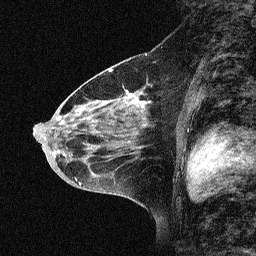
Breast MRI (dynamic contrast-enhanced), one sagittal slice; slice 35 of 64 in the series (ordered by position); dynamic contrast-enhanced study with each time point stored as its own series, time point 2 of 3 at this slice position (early post-contrast, ordered by acquisition time); 1.5 T; TE 4.5 ms, TR 11 ms; 256 × 256 image matrix, field of view 200 × 200 mm. Patient: female, 46 years. From the clinical record (not read from this slice): setting: breast cancer imaged before/during neoadjuvant chemotherapy; receptor status: HER2-positive.
Annotated regions visible in this slice (semi-automatically segmented with operator editing):
- analysis volume of interest (the breast-tissue region the enhancement analysis was run in; not a lesion): box from (x=46, y=51) to (x=180, y=169) px
- tumour enhancement mask (voxels above the 90 % enhancement threshold inside the analysis volume of interest): (x=129, y=95)–(x=146, y=105)